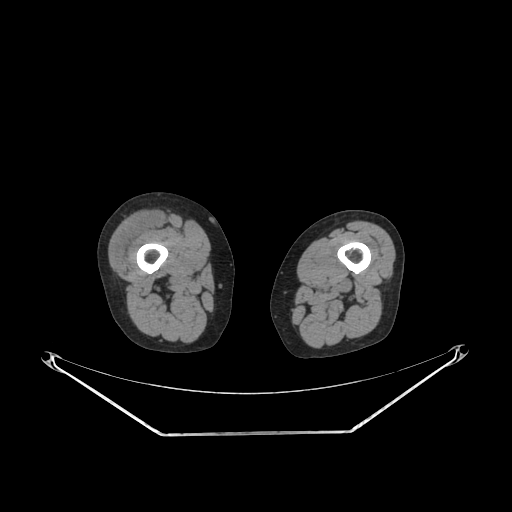
CT of an extremity soft-tissue mass (from a PET/CT study), one axial slice. Slice 210 of 311 in the series (ordered by position). Reconstruction kernel SOFT. Soft-tissue window (W 400 / L 40 HU). 3.75 mm slice thickness. 512 × 512 image matrix, field of view 500 × 500 mm. Female patient. Case-level facts recorded for this patient, not image findings: histological type: pleiomorphic undifferentiated sarcoma; grade: high; site of the primary tumour: right quadricep.
Annotated regions visible in this slice (expert contour drawn on MRI and transferred to this co-registered scan by the dataset authors):
- tumour plus oedema (research contour): box from (x=114, y=212) to (x=161, y=263) px